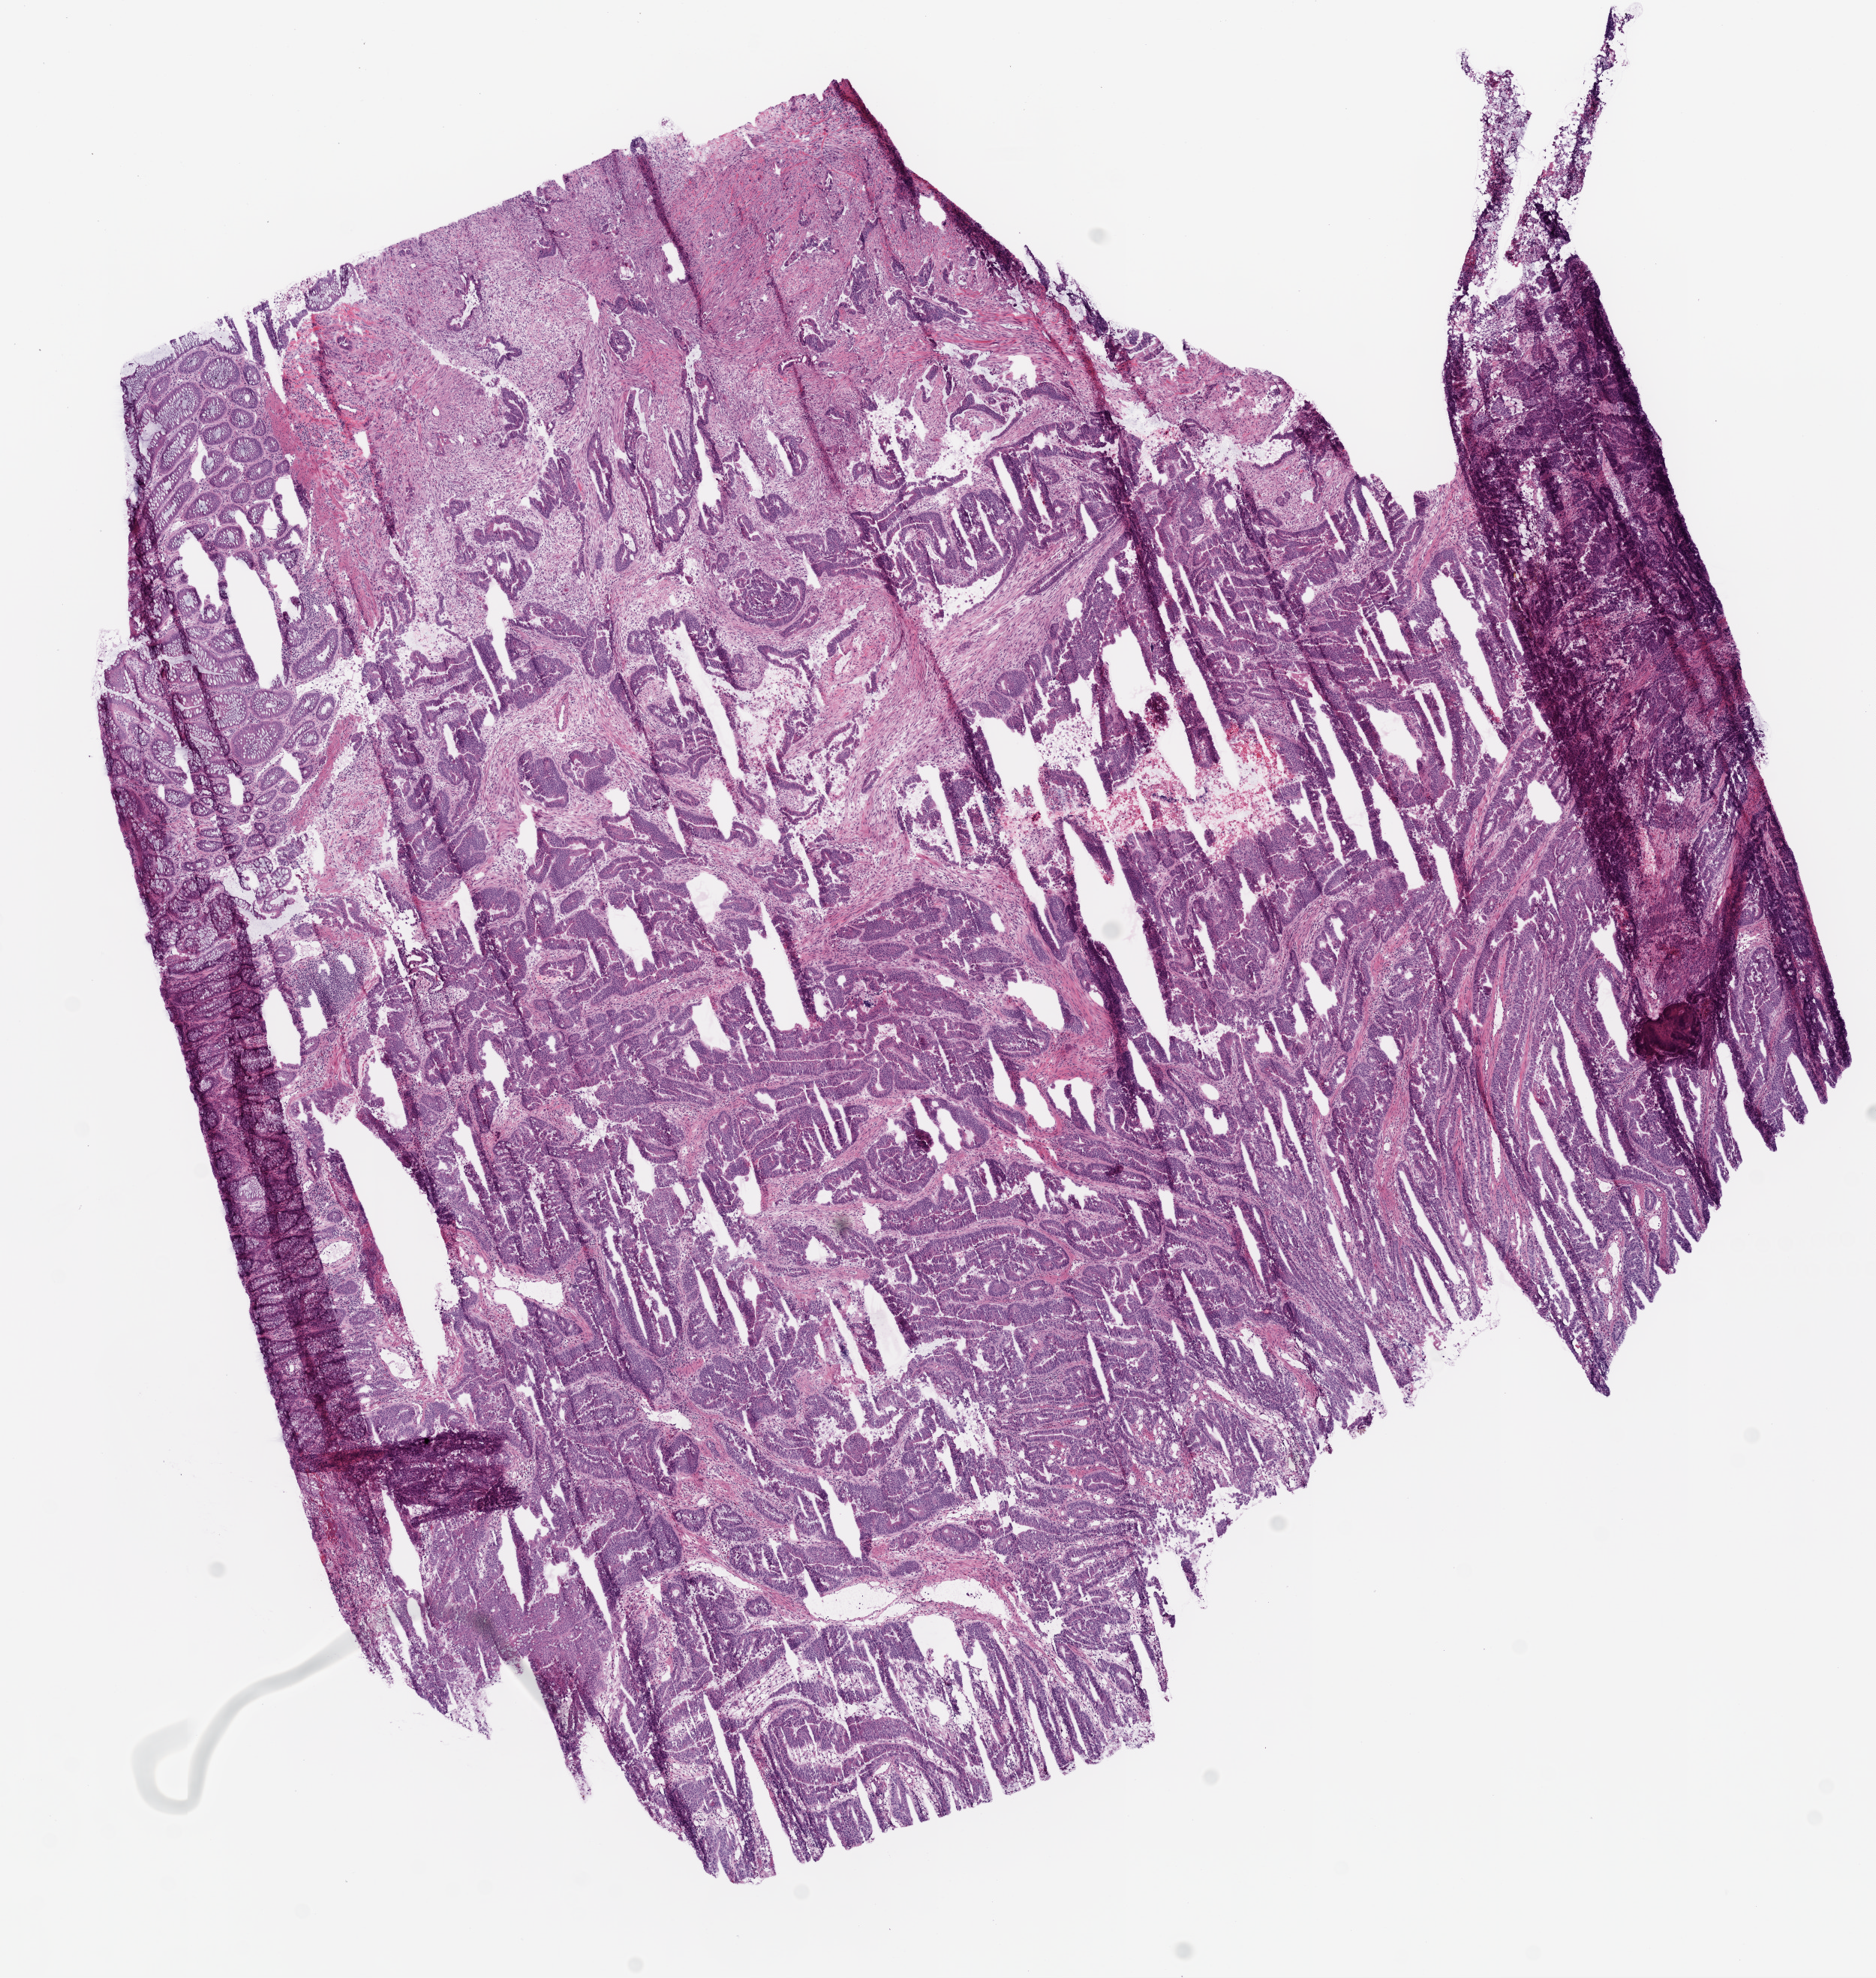
Whole-slide histology image, Hematoxylin and eosin (H&E) stained, whole scanned area (about 10.0 x 10.6 mm, from a 20x scan) shown as a low-resolution overview, frozen section from the bottom of the tissue portion, primary tumour sample from the rectum. Female, age 54 years at initial diagnosis. Pathologist review of this section (percent, as recorded): tumour cells 88%, tumour nuclei 85%, normal cells 5%, stromal cells 5%, necrosis 2%.
* AJCC pathologic stage: IIA
* lymph nodes positive (case pathology): 0 of 12 examined
* histologic diagnosis: Adenocarcinoma, NOS
* TNM: T3 N0 M0